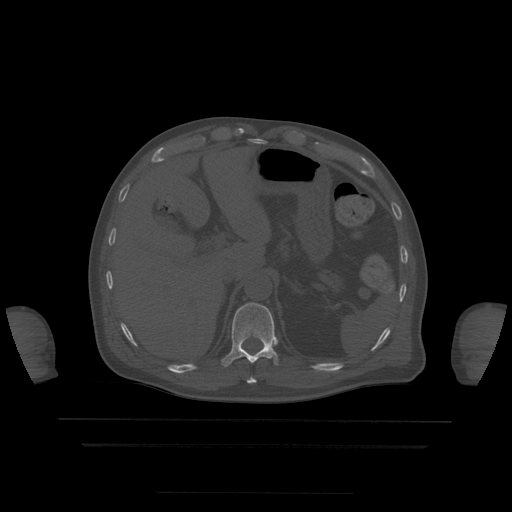
CT including the spine, one axial slice; position 220 of 522 along the scan axis; bone window (W 1800 / L 400 HU); 512 × 512 image matrix. Patient age 68 years. Case-level facts recorded for this patient, not image findings: primary cancer: urothelial.
Annotated regions visible in this slice (semi-automatic segmentation, software-assisted and operator-edited):
- T10 vertebra: bounding box <247,378,257,384> (left, top, right, bottom; pixels)
- T11 vertebra: <222,303,279,367>